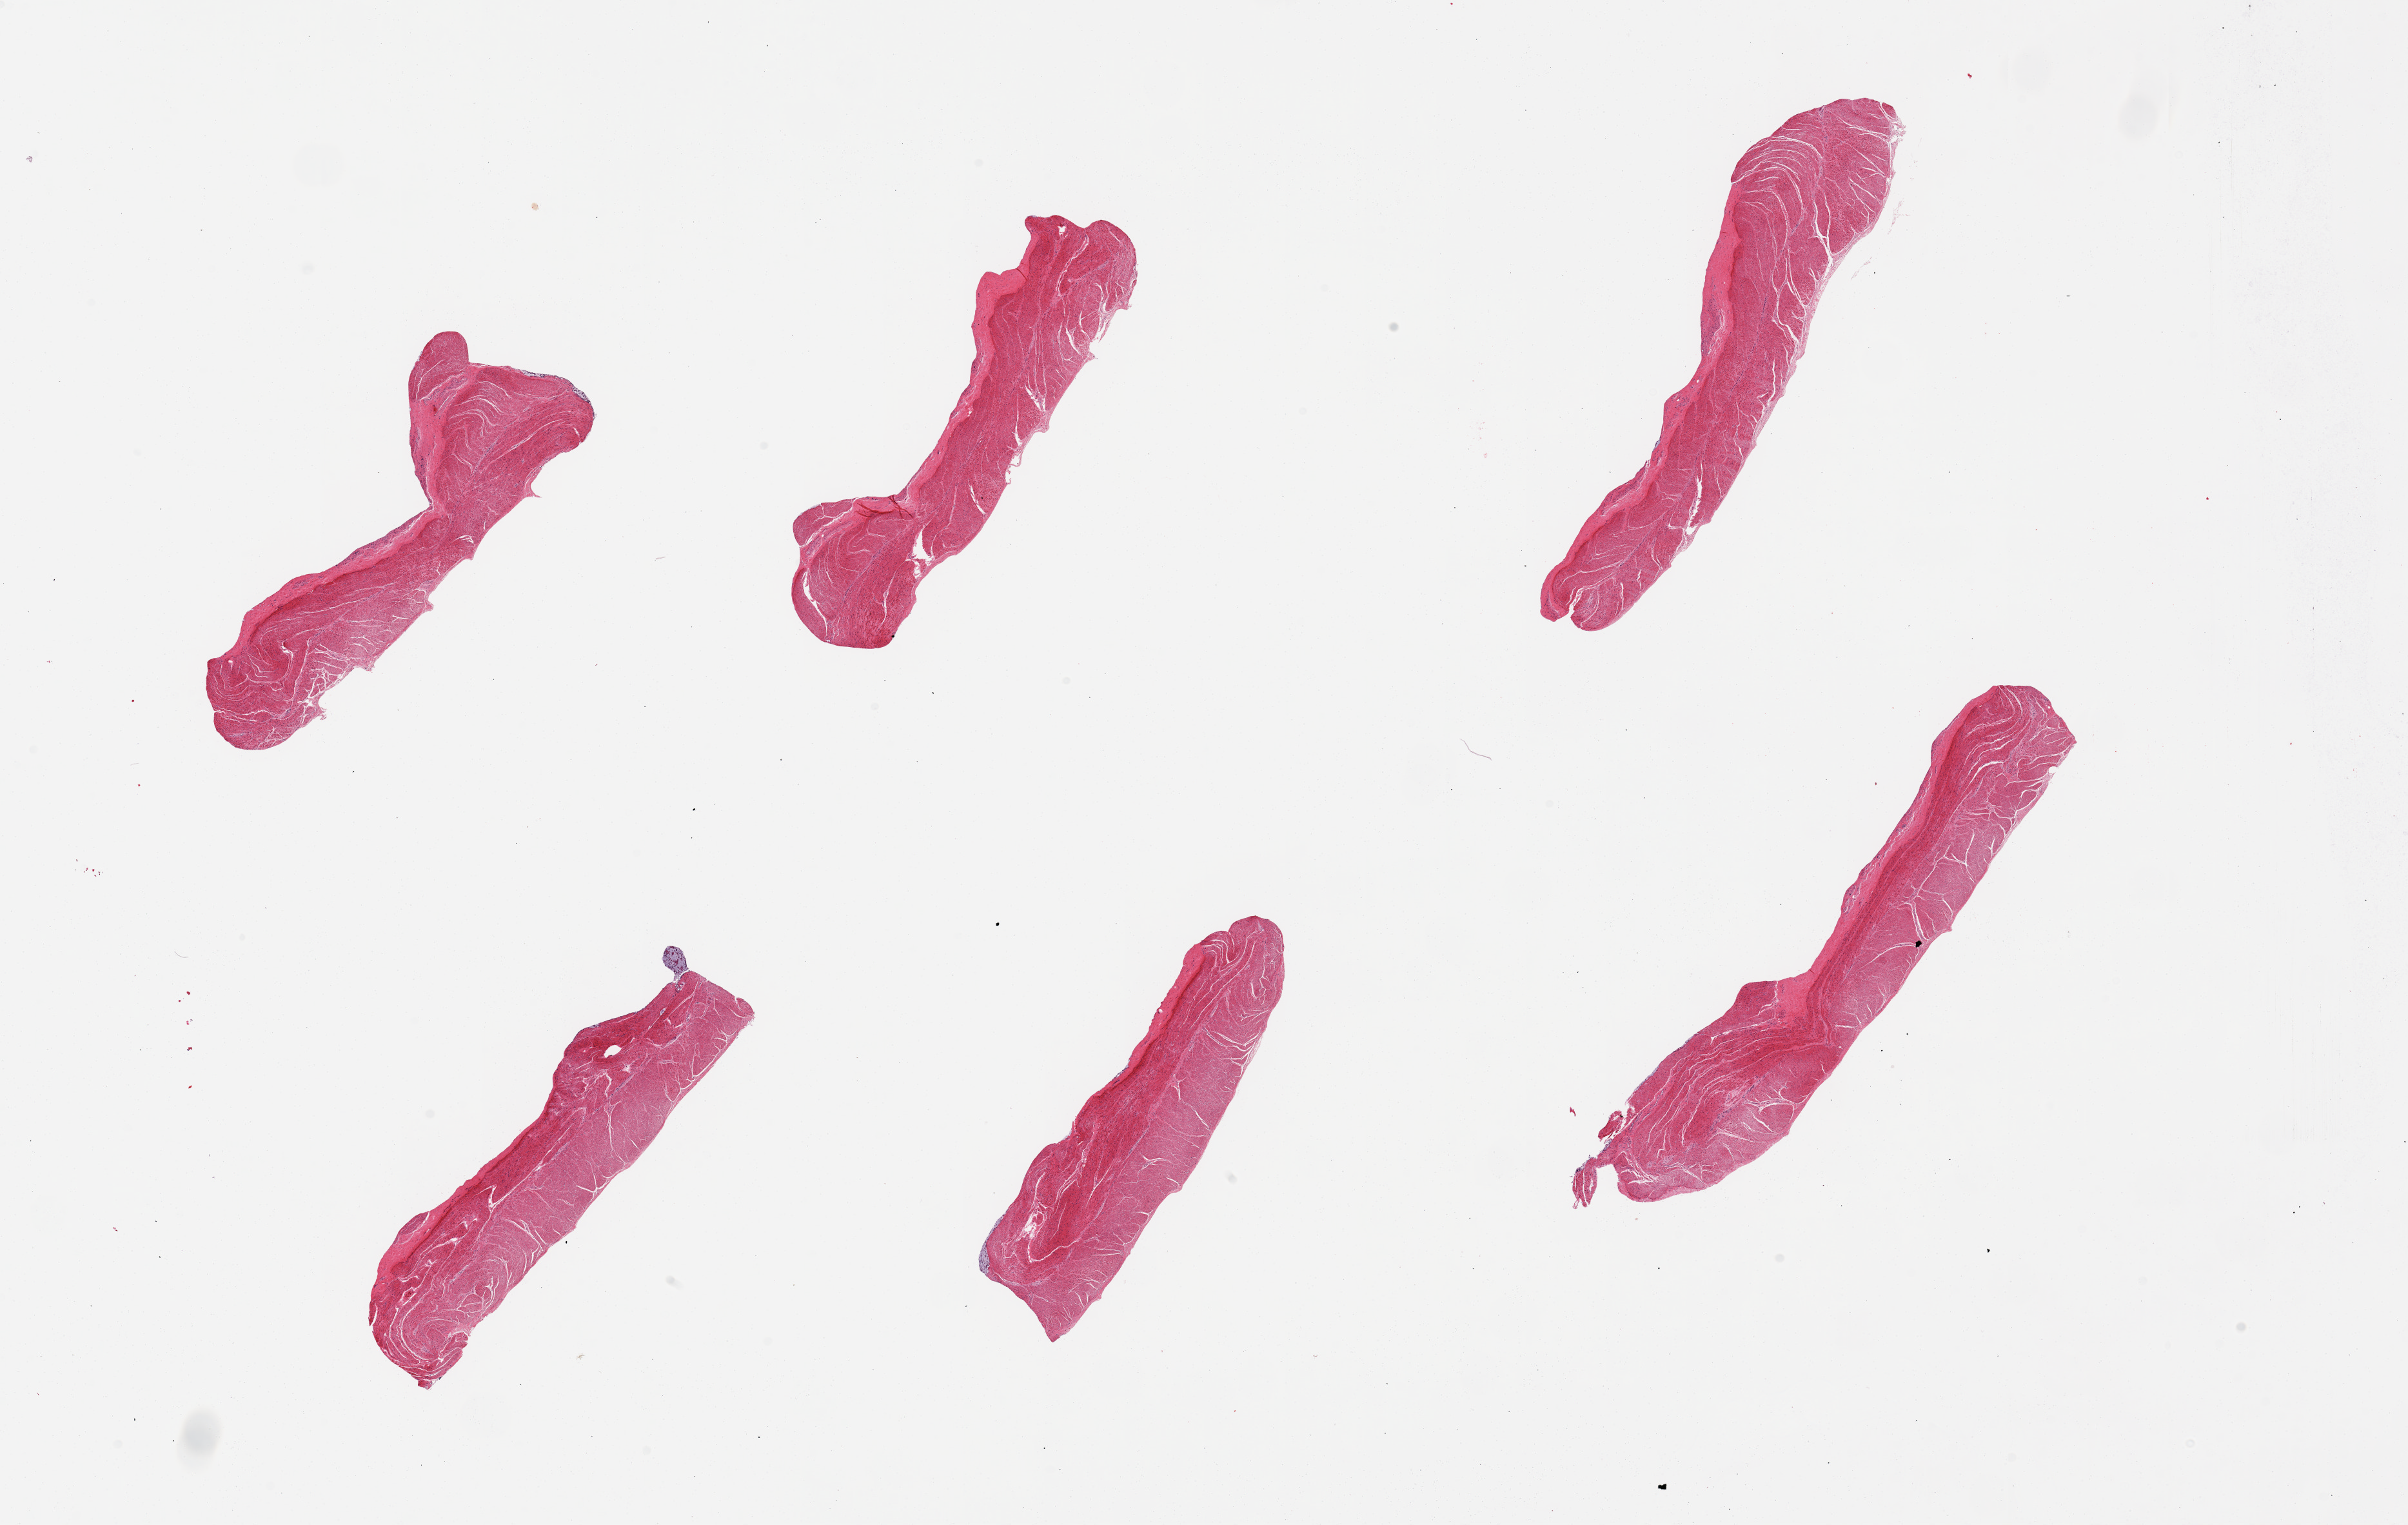
Whole-slide image, H&E stain, low-resolution overview of the scanned area, about 29.5 x 18.7 mm (from a 20x scan); PAXgene-fixed paraffin-embedded (PFPE) section; sampled site (target tissue): sigmoid colon; donor tissue sample. Male donor.
Reviewer comment on this tissue sample: 6 pieces; well trimmed.